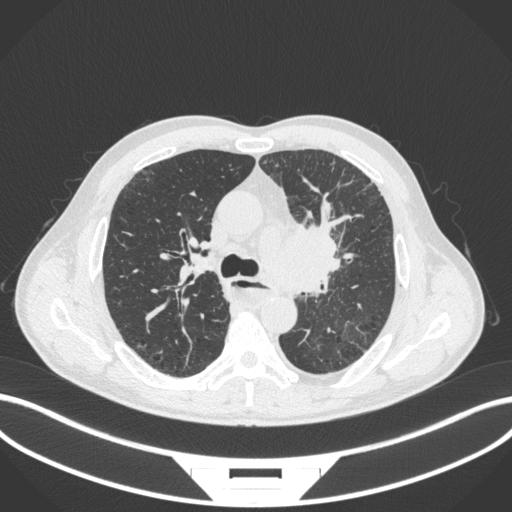
Chest CT, one axial slice. Reconstruction kernel B31f. 120 kVp. Lung window (W 1500 / L -600 HU). 512 × 512 image matrix, field of view 400 × 400 mm. Male patient, age 57 years. Case-level facts recorded for this patient, not image findings: clinical TNM (as recorded): T2a N1 M0.
Annotated regions visible in this slice (rectangle marked by the reading radiologist):
- lung tumour (recorded histology: squamous cell carcinoma): box from (x=258, y=214) to (x=347, y=299) px